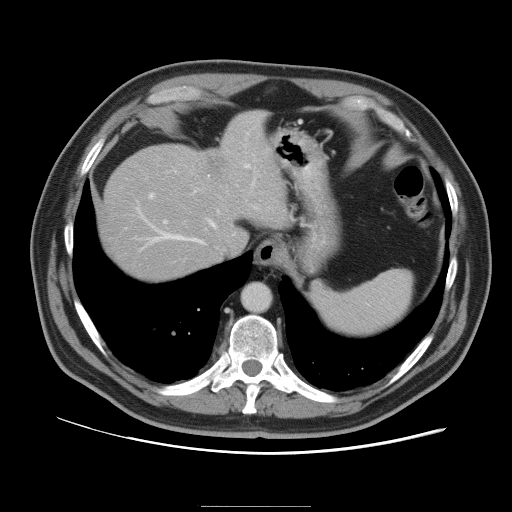
Contrast-enhanced abdominal CT, one axial slice. Slice 82 of 105 in the series (ordered by position). 120 kVp. Intravenous contrast given. Soft-tissue window (W 400 / L 40 HU). 5 mm slice thickness. 512 × 512 image matrix. Male patient, age 64 years. Case-level facts recorded for this patient, not image findings: diagnosis: colorectal cancer liver metastases, imaged before liver resection; multiple liver metastases: yes; largest metastasis: 3 cm.
Annotated regions visible in this slice (outlined manually by an expert reader):
- hepatic veins: bounding box [x1, y1, x2, y2] px = [138, 178, 256, 244]
- liver: [102, 112, 285, 280]
- planned liver remnant (the part of the liver to remain after resection): [102, 151, 232, 278]
- portal vein (with intrahepatic branches): [148, 164, 251, 224]
- liver metastasis: [207, 157, 226, 178]